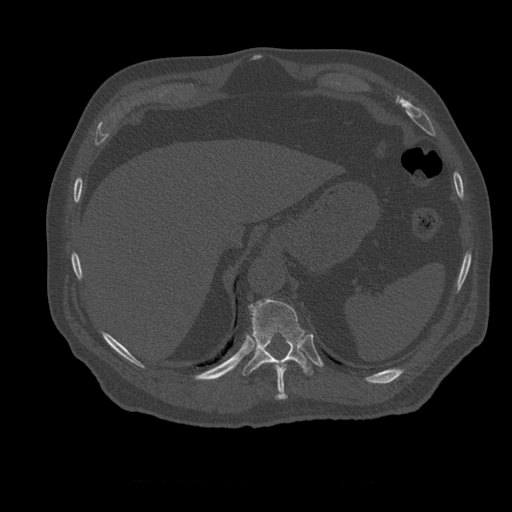
CT including the spine, one axial slice. Position 286 of 399 along the scan axis. 120 kVp. Bone window (W 1800 / L 400 HU). 1.25 mm slice thickness. 512 × 512 image matrix, field of view 407 × 407 mm. Patient age 73 years. Case-level facts recorded for this patient, not image findings: primary cancer: prostate; vertebrae with lytic lesions (as recorded): L2.
Outlined on this slice (semi-automatically segmented with operator editing):
- T10 vertebra: bounding box <272,361,287,400> (left, top, right, bottom; pixels)
- T11 vertebra: <243,298,313,376>